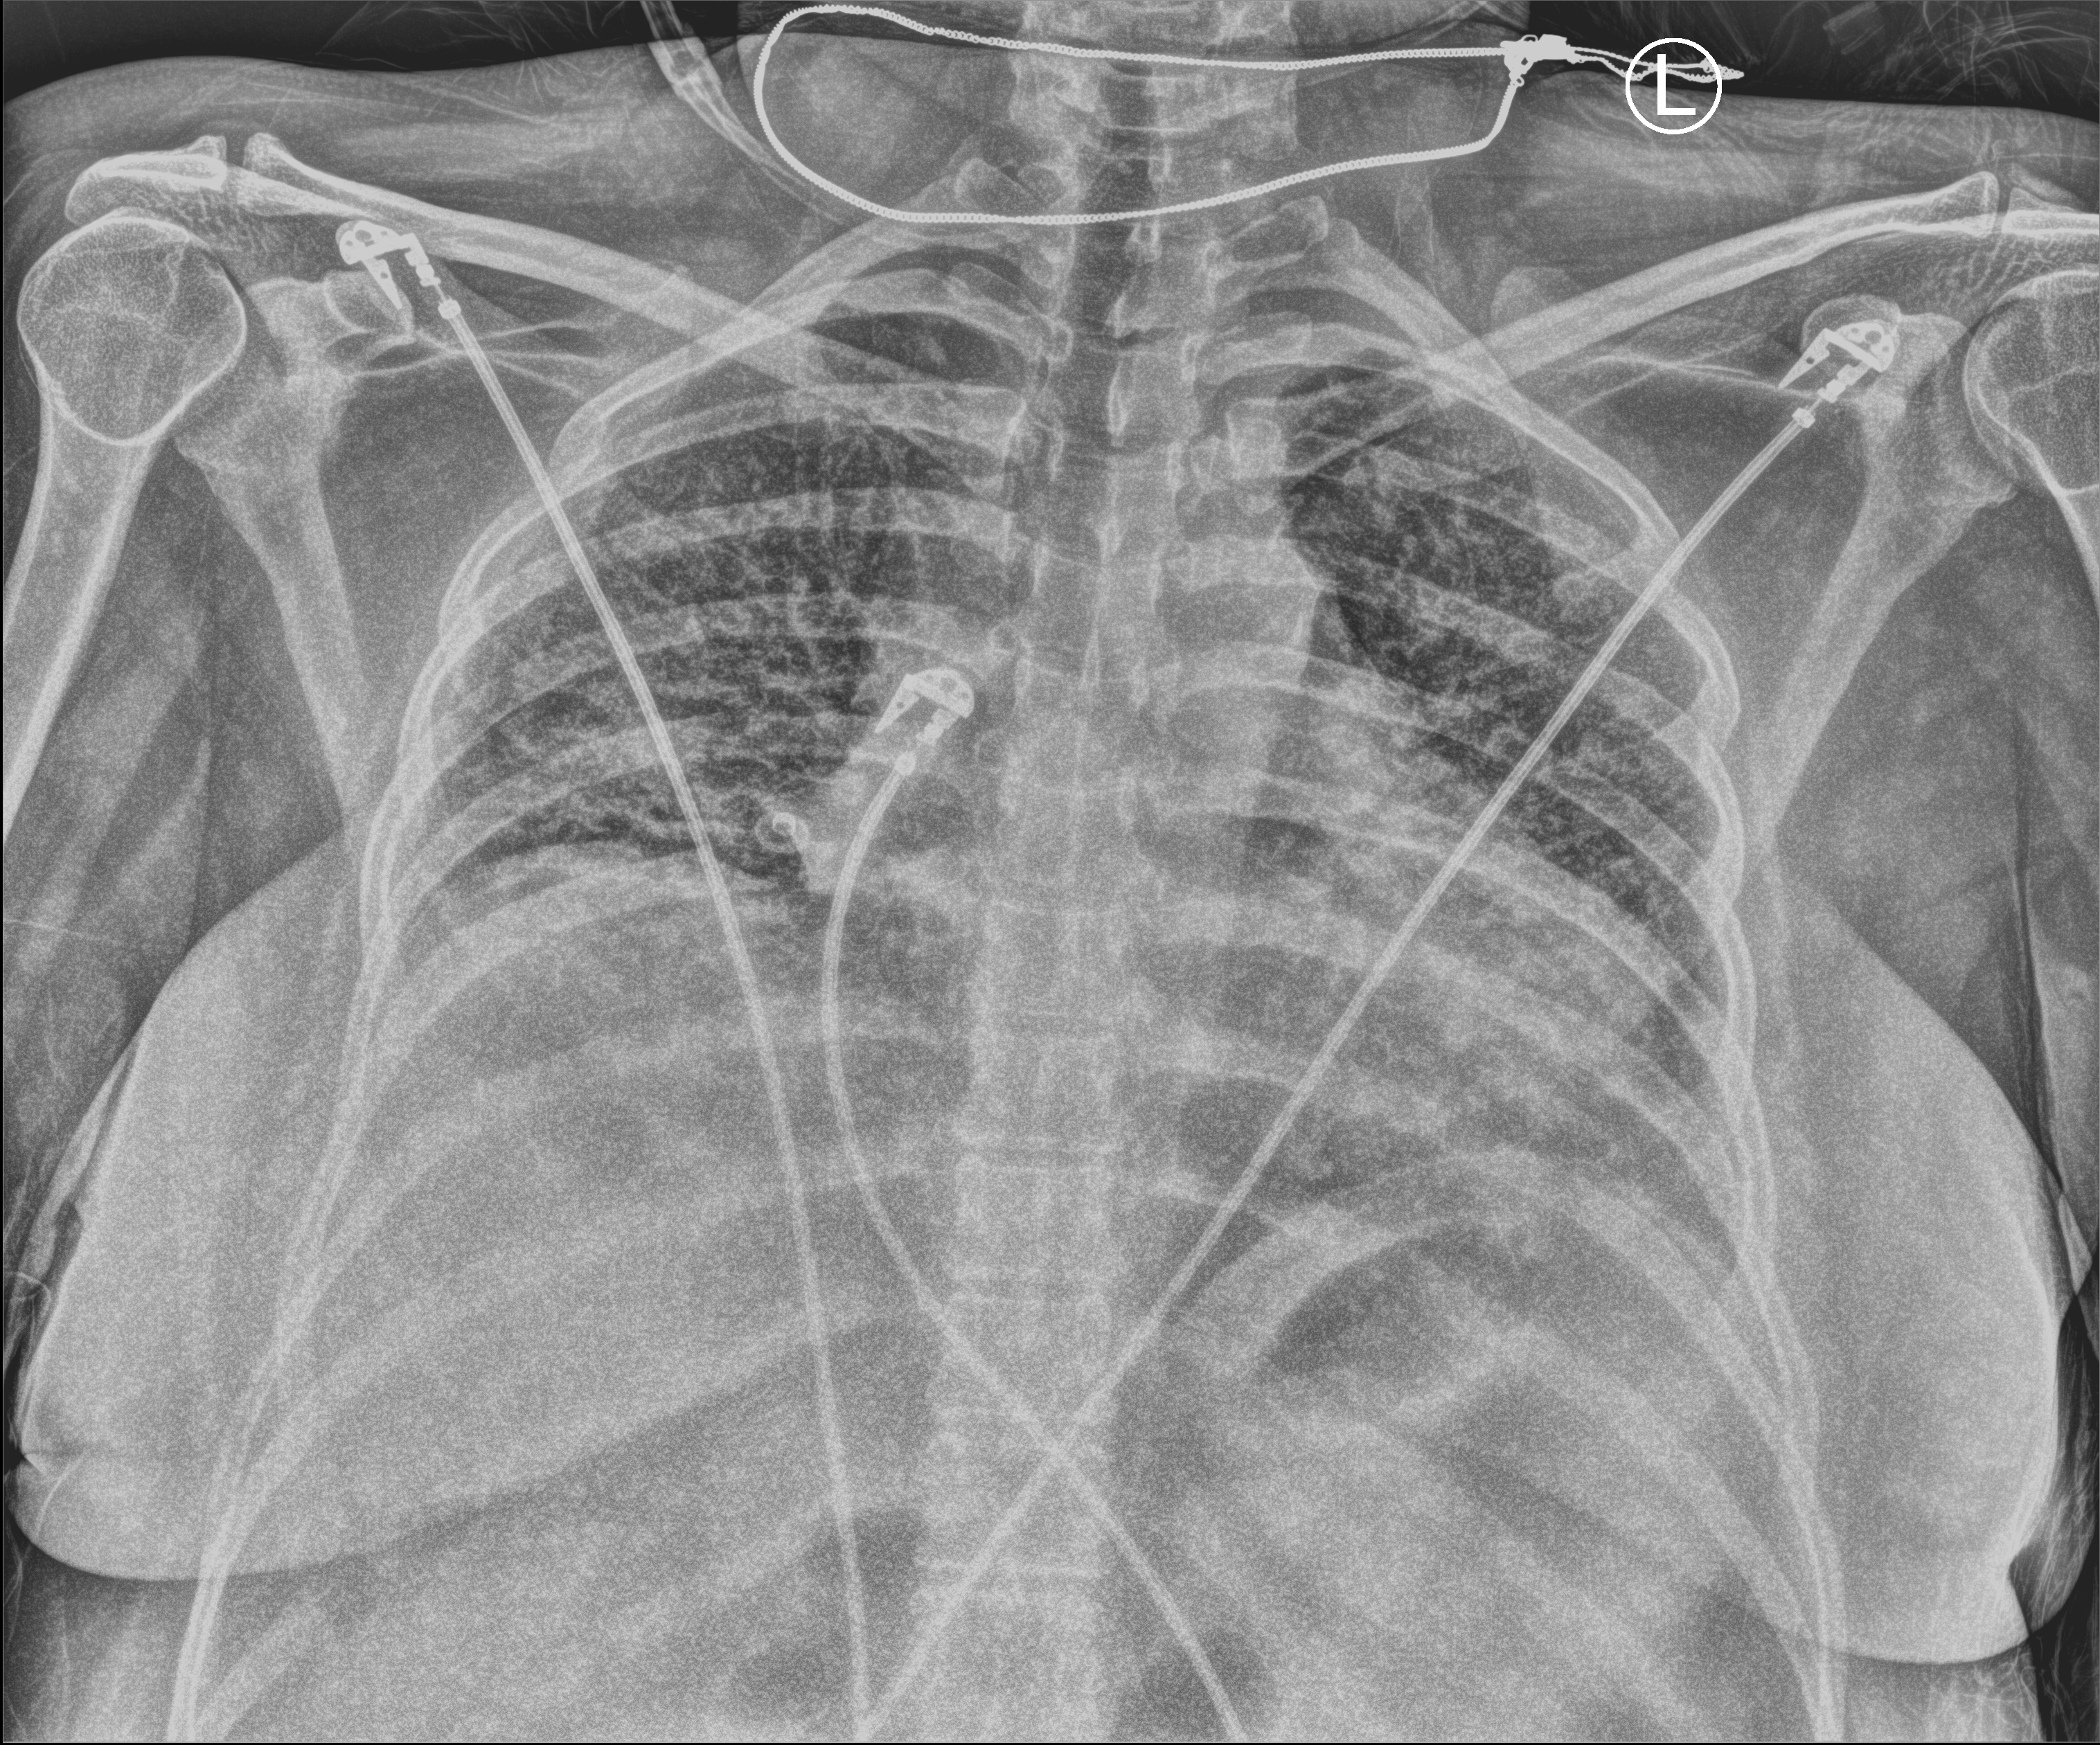
Bedside chest radiograph (computed radiography), anteroposterior (AP) projection. Female patient hospitalised with COVID-19, age 18–59 years.
From the hospital-stay record, not from the radiograph (when in the stay this image was taken is not recorded): admitted to intensive care during this hospital stay: yes; mechanically ventilated during this hospital stay: yes; diabetes (admission record): no.